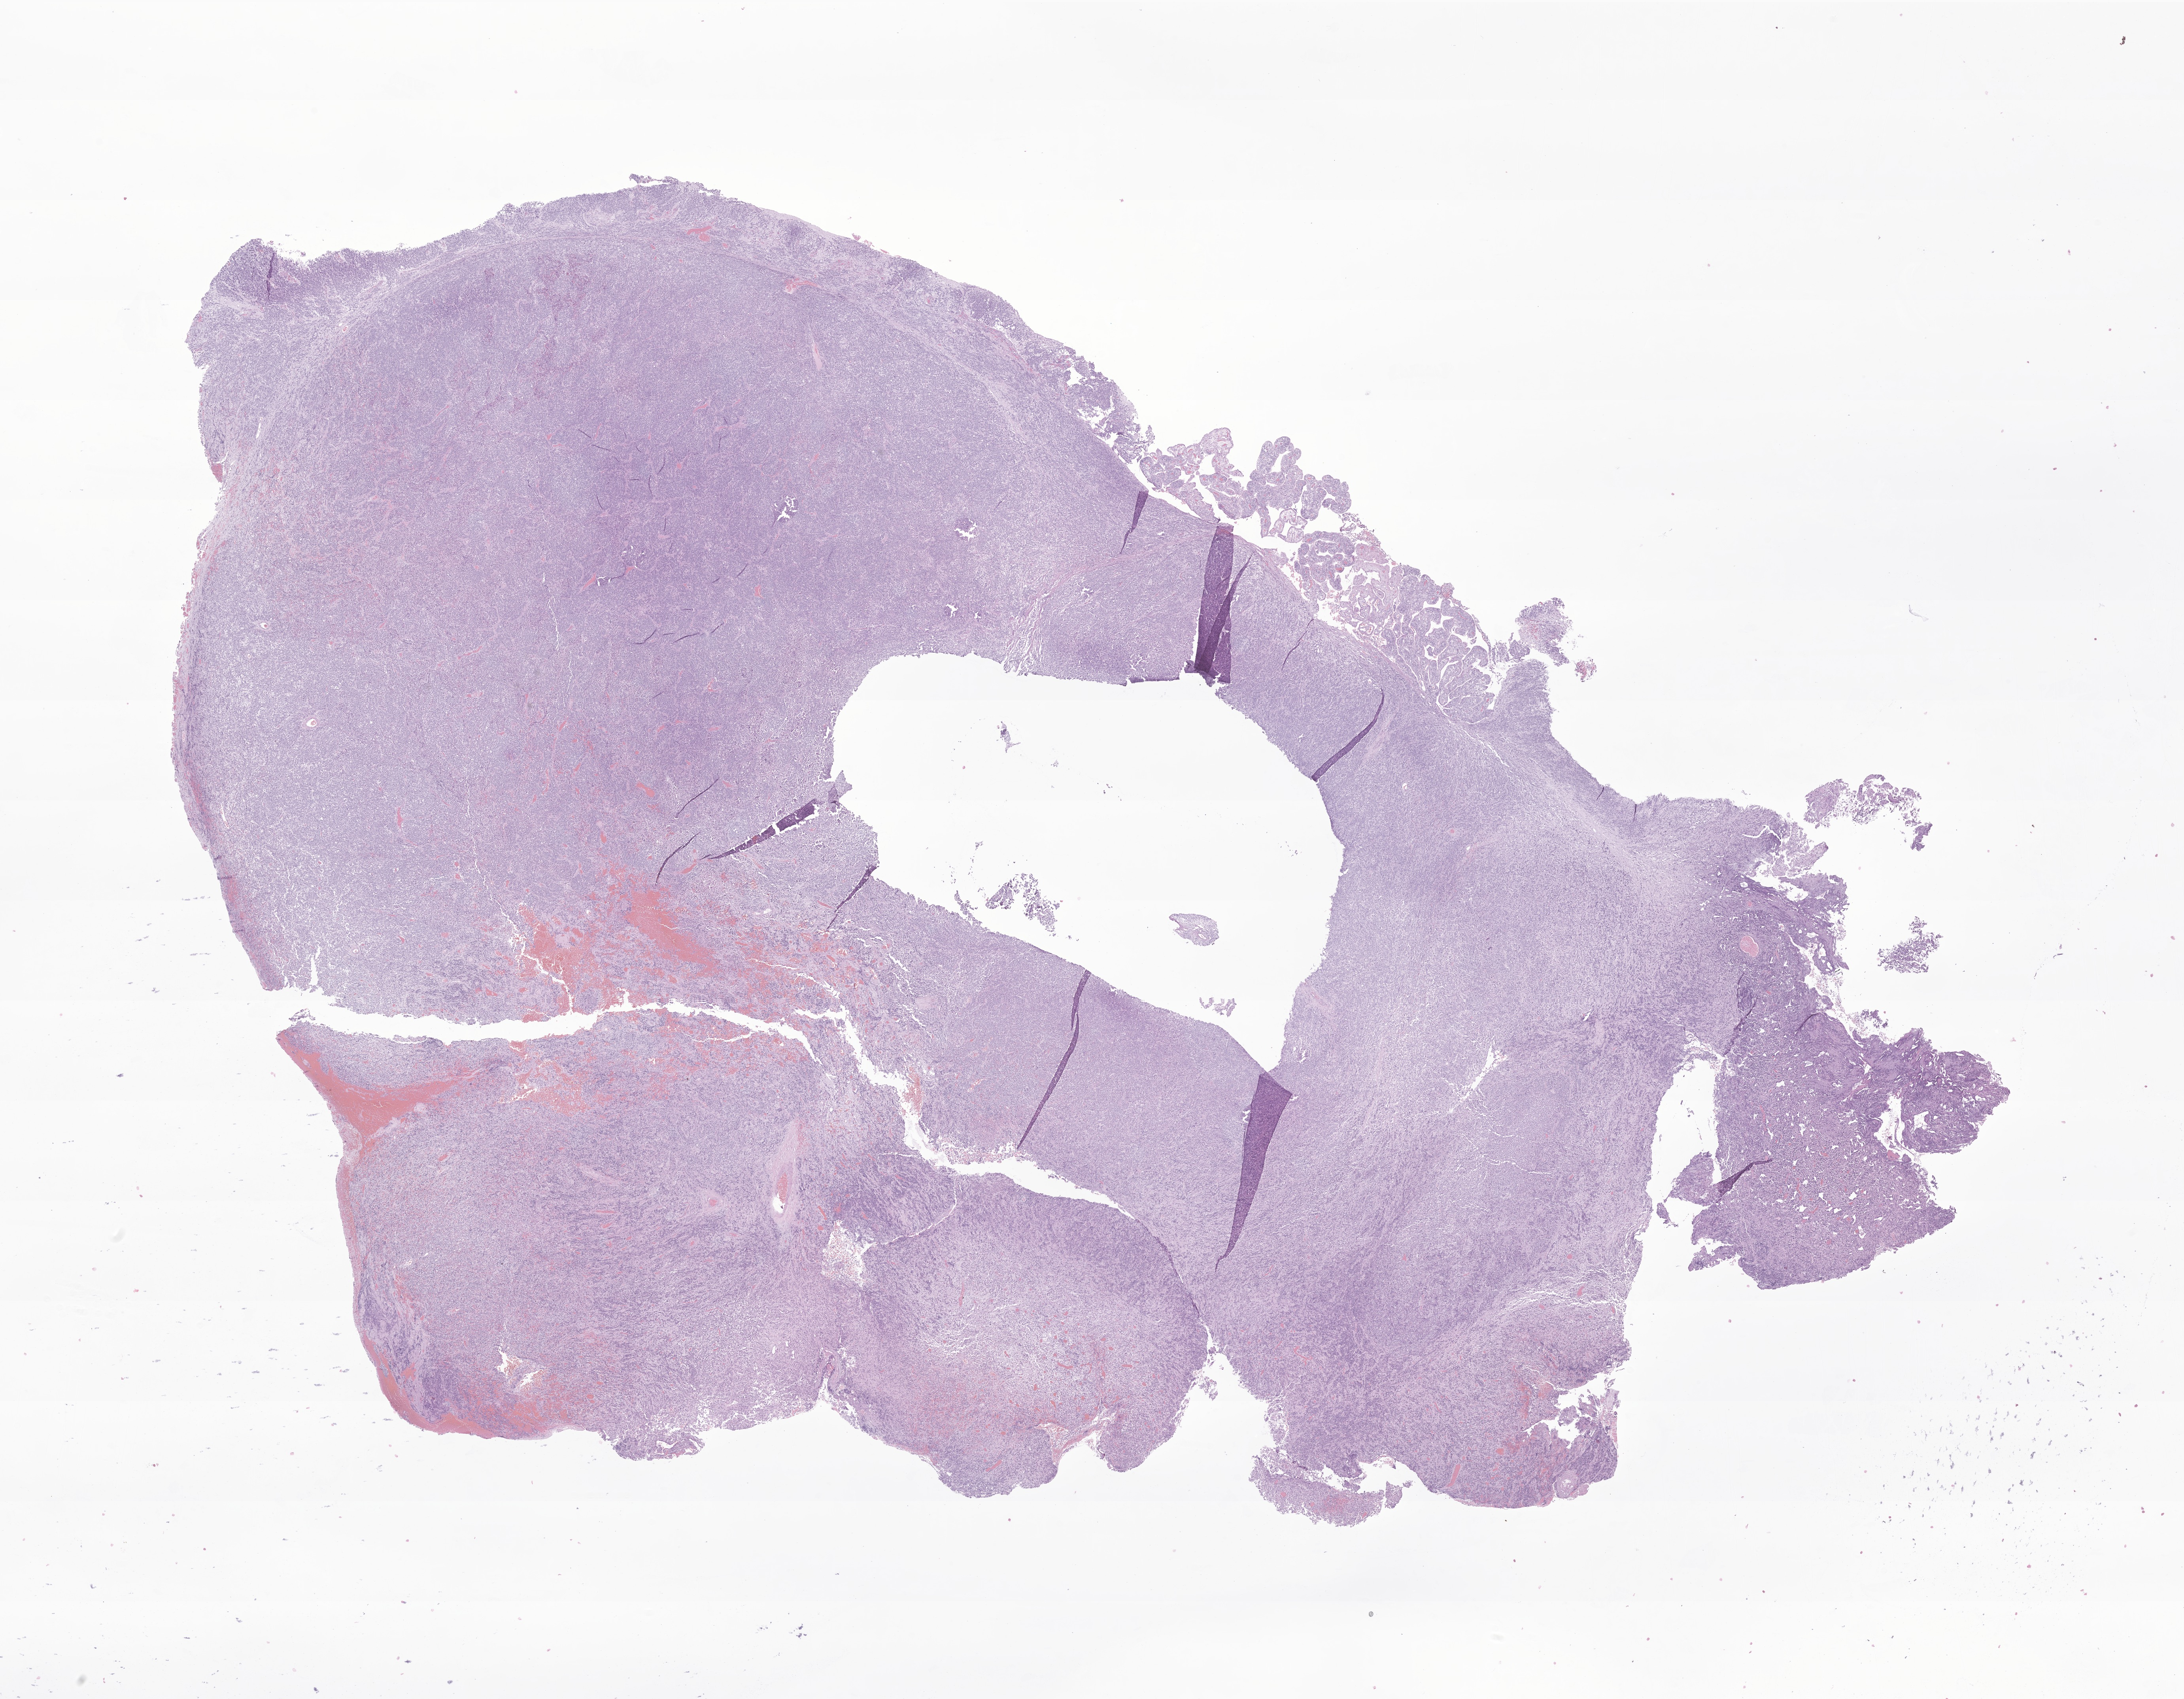
Haematoxylin and eosin whole-slide image of tumor tissue from the brain stem — low-resolution overview of the scanned area, about 23.3 x 18.1 mm; formalin-fixed, paraffin-embedded (FFPE) tissue. Patient: female, age 46 months (3 years 10 months).
Diagnosis: Medulloblastoma, NOS.